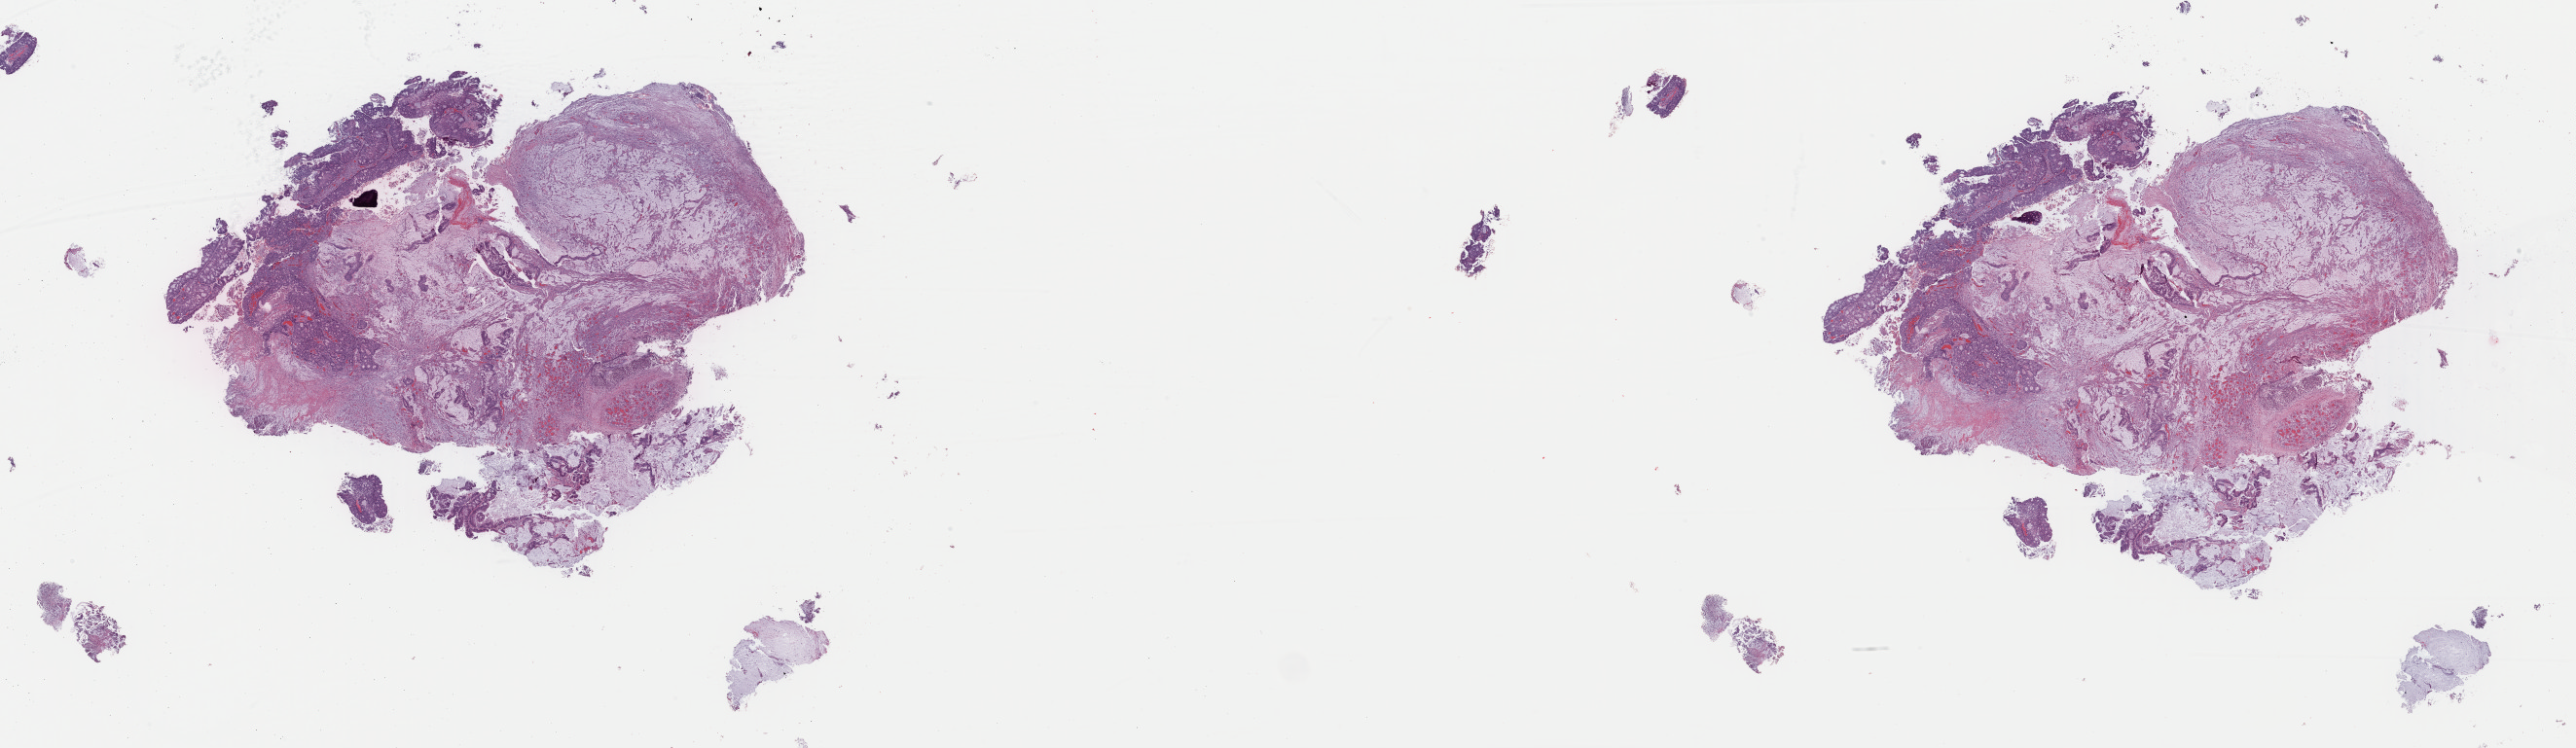
Whole-slide histology image, H&E-stained, whole scanned area (about 41.8 x 12.1 mm, from a 40x scan) shown as a low-resolution overview. Formalin-fixed paraffin-embedded (FFPE) diagnostic section. Primary tumour sample from the colon. Female, age 55 years at initial diagnosis.
Pathologic diagnosis: Mucinous adenocarcinoma.